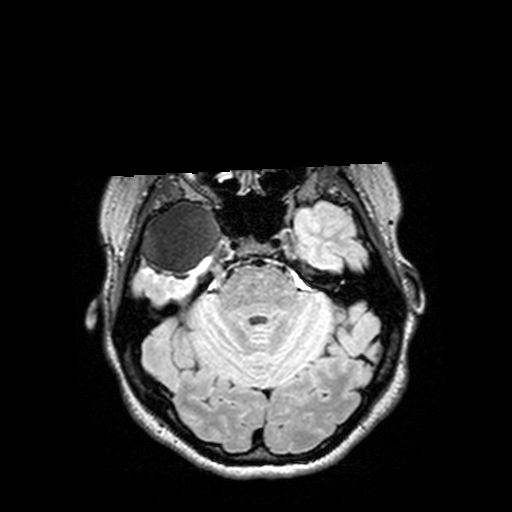
Brain MRI from a brain-tumour surgery series, one axial slice. Position 102 of 144 along the scan axis. T2 FLAIR. 1 mm slice thickness. 512 × 512 image matrix, field of view 250 × 250 mm. From the clinical record (not read from this slice): histopathology: Astrocytoma; WHO grade: 3; IDH mutation: yes.
Outlined on this slice (outlined manually by an expert reader):
- tumour: bounding box [x1, y1, x2, y2] px = [126, 199, 232, 280]